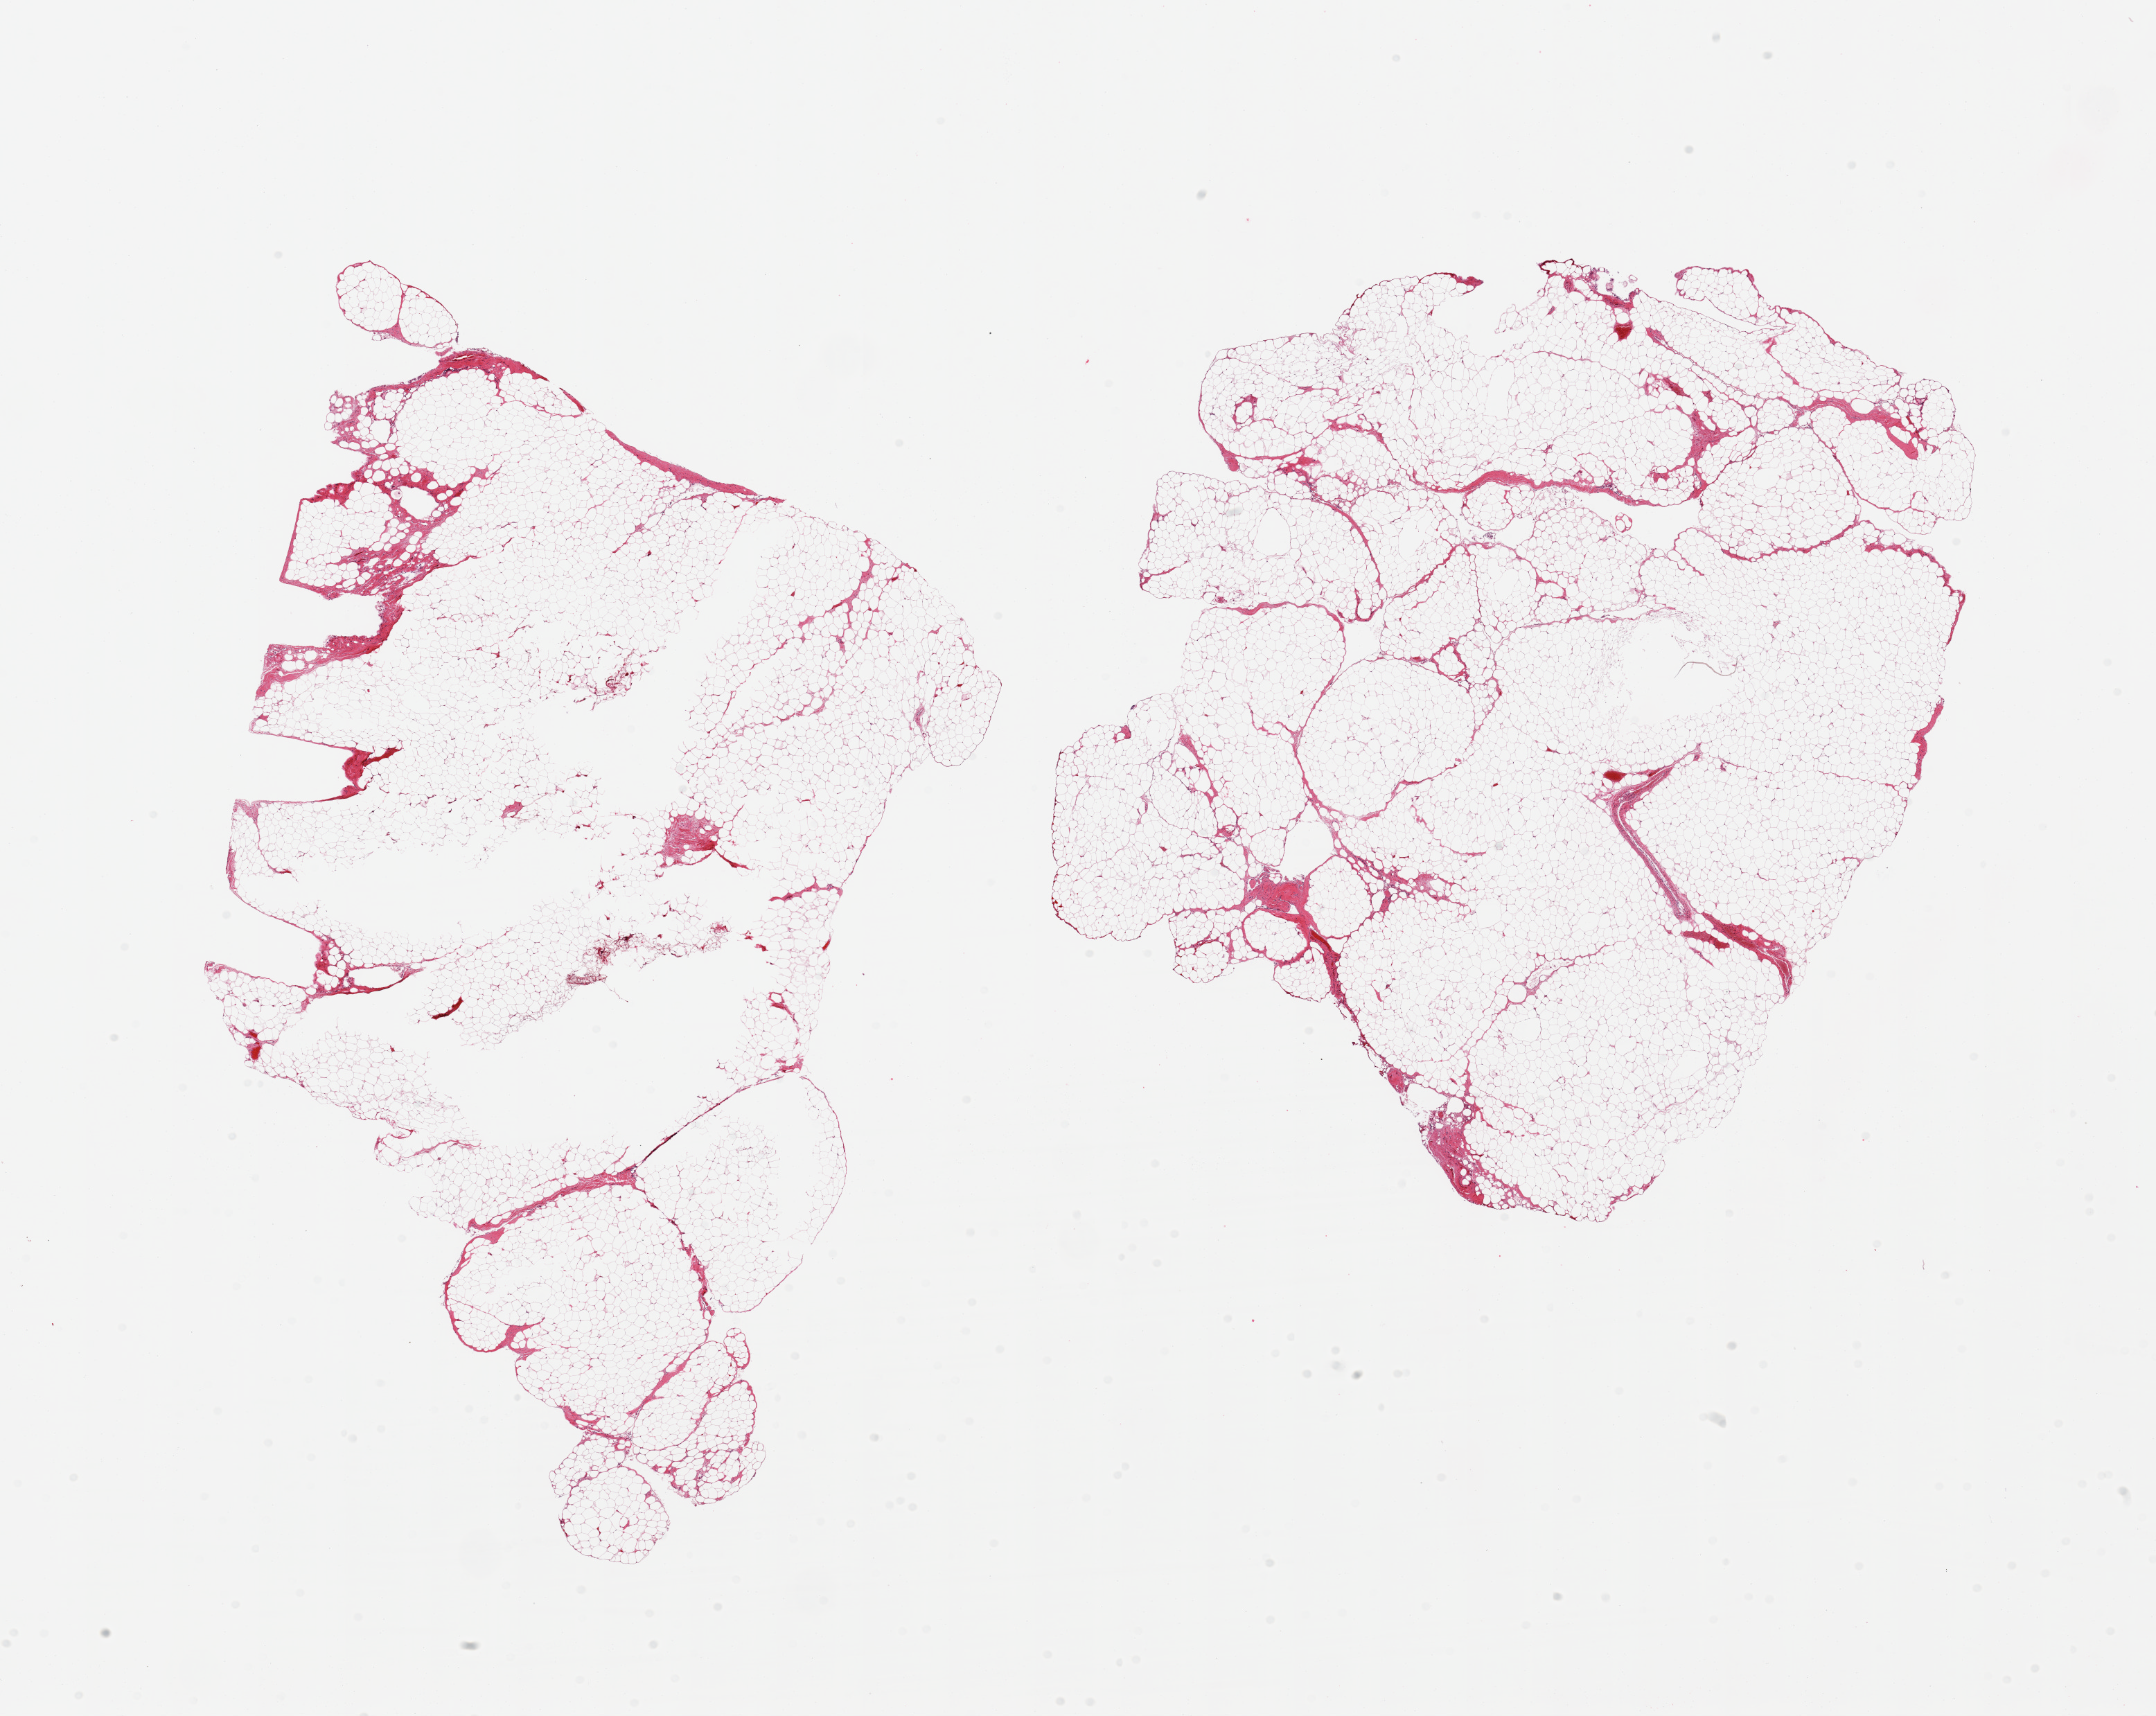
Digitized hematoxylin and eosin (H&E)-stained section — low-resolution overview of the scanned area, about 24.6 x 19.6 mm; PAXgene-fixed, paraffin-embedded tissue; sampled site (target tissue): omentum; donor tissue sample. Donor sex: male.
Review note (as recorded): 2 pieces, ~5-10% fascia/vascular elements.